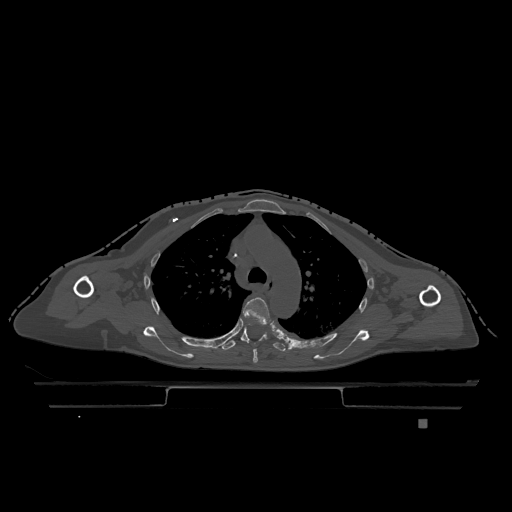
CT including the spine, one axial slice. Position 858 of 1317 along the scan axis. Bone window (W 1800 / L 400 HU). 0.5 mm slice thickness. 512 × 512 image matrix, field of view 500 × 500 mm. Female patient, age 74 years. Case-level facts recorded for this patient, not image findings: primary cancer: lung.
Structures marked on this image (semi-automatically segmented with operator editing):
- T4 vertebra: bounding box [x1, y1, x2, y2] px = [243, 297, 271, 363]
- T5 vertebra: [222, 323, 287, 352]